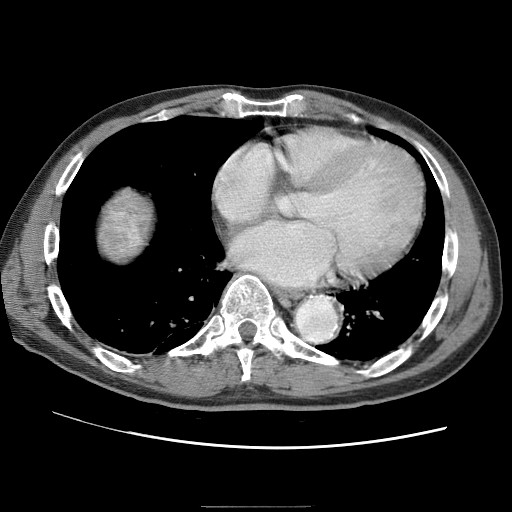
Contrast-enhanced abdominal CT (liver protocol), one axial slice; slice 71 of 75 in the series (ordered by position); reconstruction kernel STANDARD; one of 2 acquisitions stored at this slice position; soft-tissue window (W 400 / L 40 HU); 512 × 512 image matrix, field of view 360 × 360 mm. Case-level facts recorded for this patient, not image findings: diagnosis: hepatocellular carcinoma (patient treated with transarterial chemoembolisation; whether this scan precedes or follows treatment is not stated here); TNM stage (as recorded): Stage-II; Child-Pugh class: A; tumour nodularity: multinodular.
Structures marked on this image (semi-automatically segmented with operator editing):
- liver parenchyma outside the tumour (the mass and vessels are separate outlines, so this box may not span the whole liver): box from (x=88, y=174) to (x=174, y=270) px
- mass: (x=88, y=177)–(x=153, y=269)